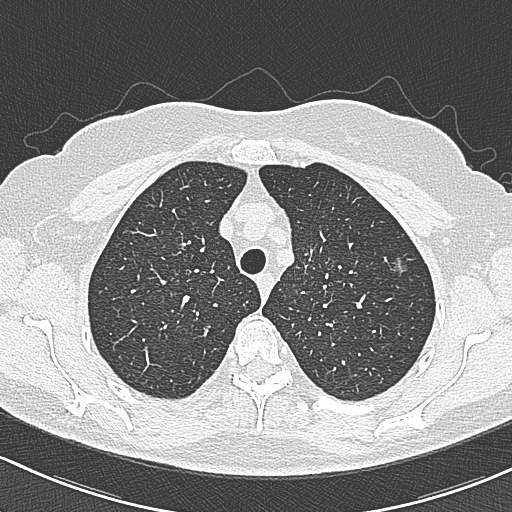
Axial slice from a low-dose chest CT screening exam, baseline screening round, lung window (W 1500 / L -600 HU), 1 mm slice thickness, lung (sharp) reconstruction kernel (B80f), 120 kVp, slice 66 of 312 in the series. Female, age 65 years at enrolment.
- Lesion marked by an expert reader, bounding box [x1, y1, x2, y2] px = [384, 255, 419, 287].
- The screening reader recorded 3 non-calcified nodules or masses ≥4 mm on this exam (left upper lobe, left upper lobe, right upper lobe); which of them this box marks is not recorded.